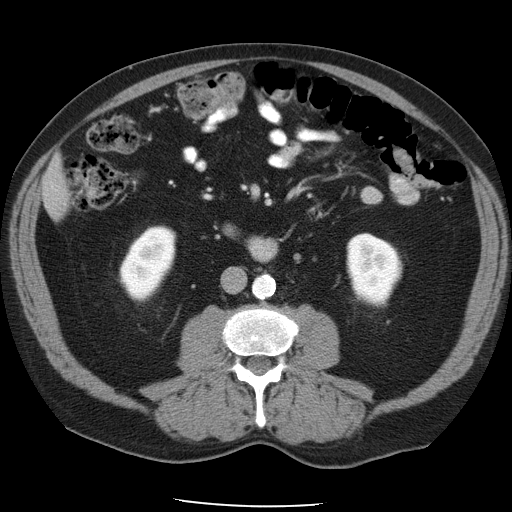
Contrast-enhanced abdominal CT, one axial slice. Slice 13 of 49 in the series (ordered by position). Reconstruction kernel STANDARD. Soft-tissue window (W 400 / L 40 HU). 5 mm slice thickness. 512 × 512 image matrix, field of view 395 × 395 mm. Male patient, age 68 years. Case-level facts recorded for this patient, not image findings: diagnosis: colorectal cancer liver metastases, imaged before liver resection; multiple liver metastases: yes; largest metastasis: 1.7 cm.
Structures marked on this image (outlined manually by an expert reader):
- liver: bounding box [x1, y1, x2, y2] px = [45, 164, 67, 213]